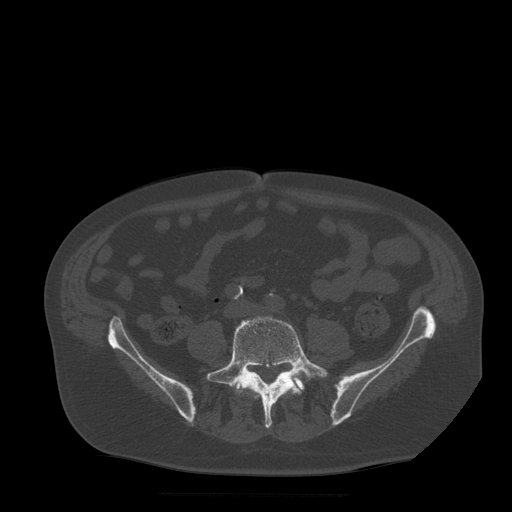
CT including the spine, one axial slice; slice 90 of 522 in the series (ordered by position); bone window (W 1800 / L 400 HU); 1.25 mm slice thickness; 512 × 512 image matrix, field of view 420 × 420 mm. Patient age 72 years. From the clinical record (not read from this slice): primary cancer: prostate.
Structures marked on this image (semi-automatically segmented with operator editing):
- L5 vertebra: bounding box [x1, y1, x2, y2] px = [206, 315, 328, 428]